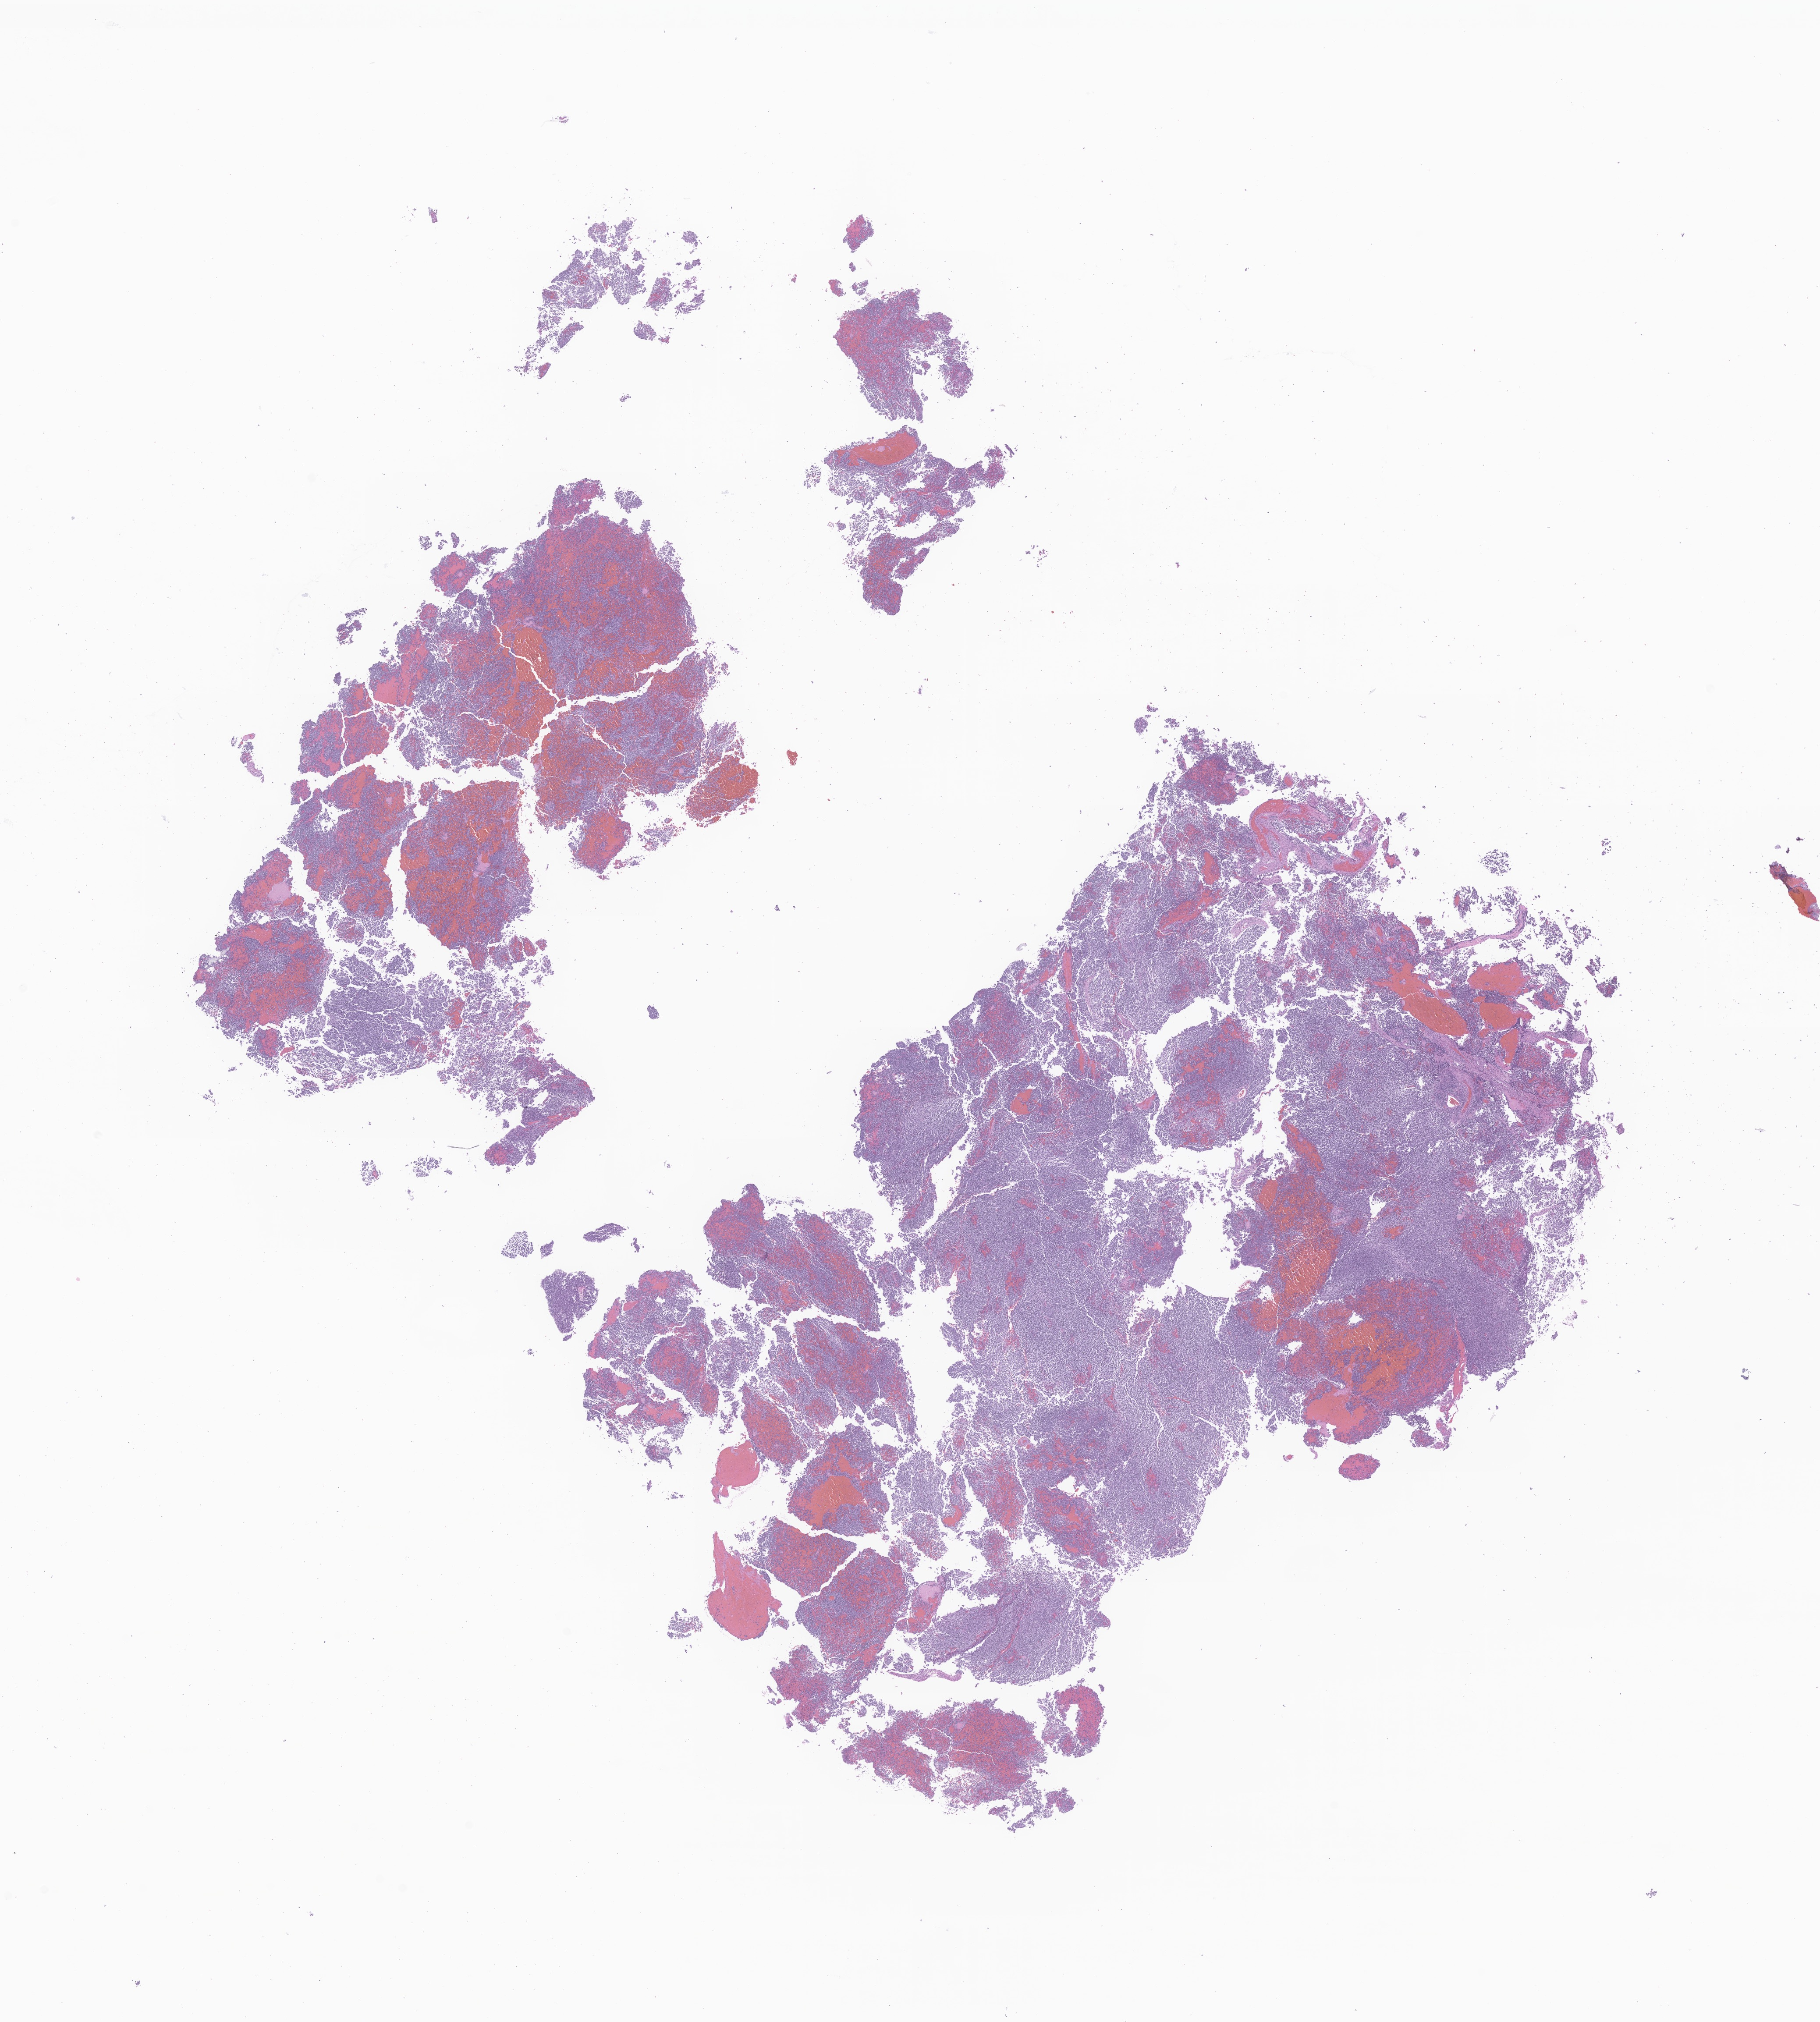
Digitized H&E-stained section of tumor tissue from the brain — low-resolution overview of the scanned area, about 17.5 x 19.4 mm. Formalin-fixed paraffin-embedded section. Patient male; age 51 months (4 years 3 months).
Diagnosis (ICD-O-3 morphology term): Medulloblastoma, NOS.